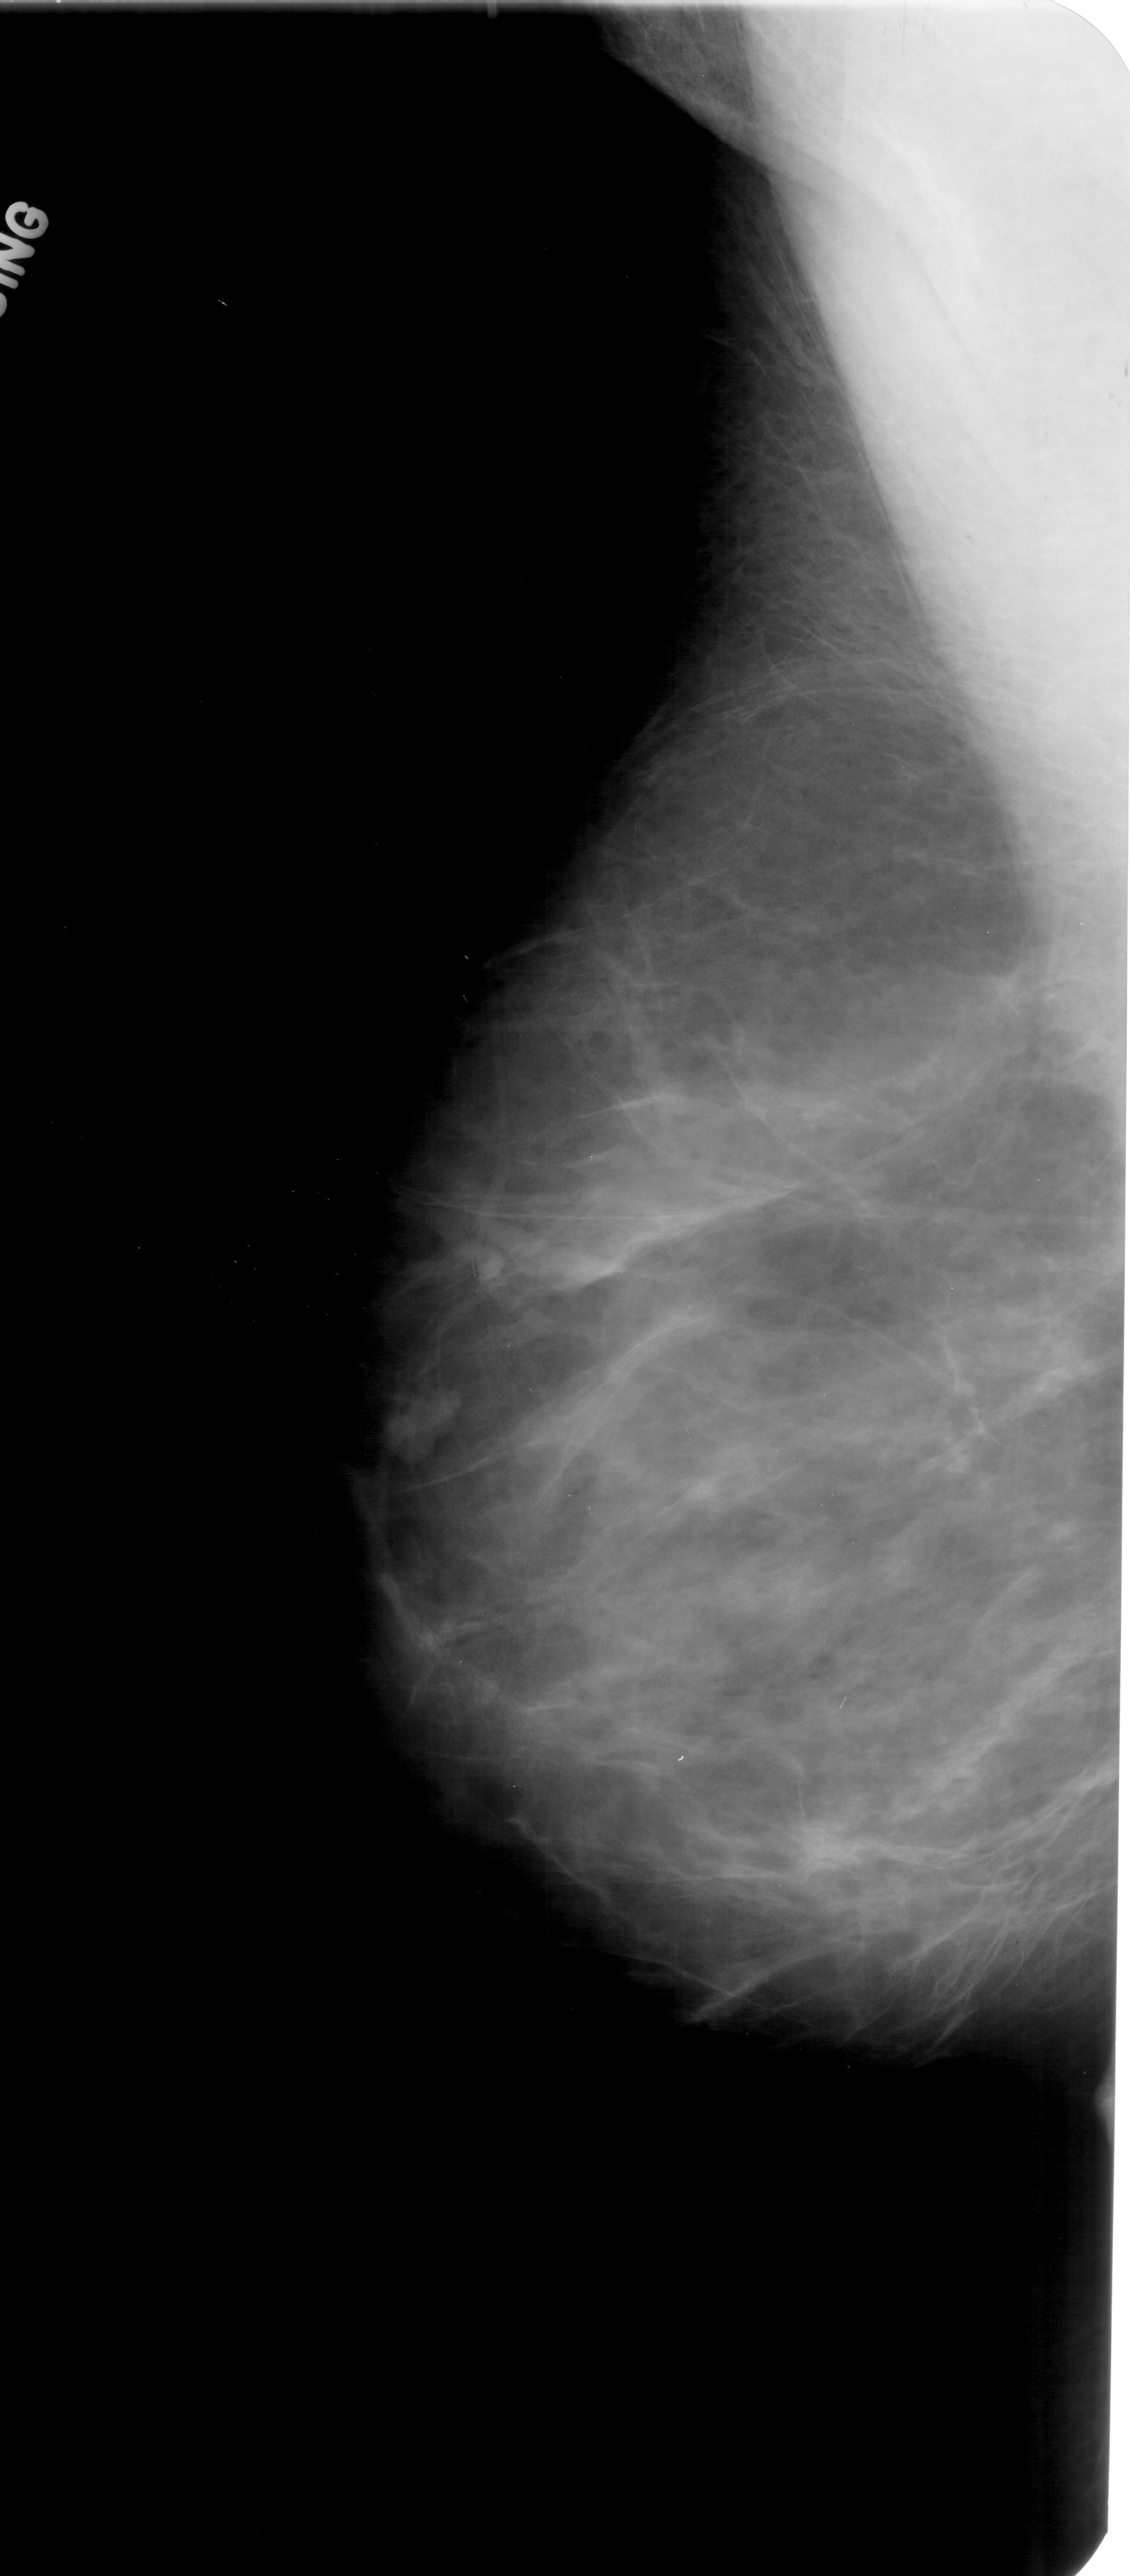
Digitized screen-film mammogram; left breast; MLO view; 1130 × 2576 image matrix.
Expert-marked regions of interest on this image (one box per marked abnormality):
- mass, shape lobulated, margins circumscribed; BI-RADS assessment category 4; pathology result (as recorded, not read from the image): benign: bounding box <379,1379,466,1453> (left, top, right, bottom; pixels)